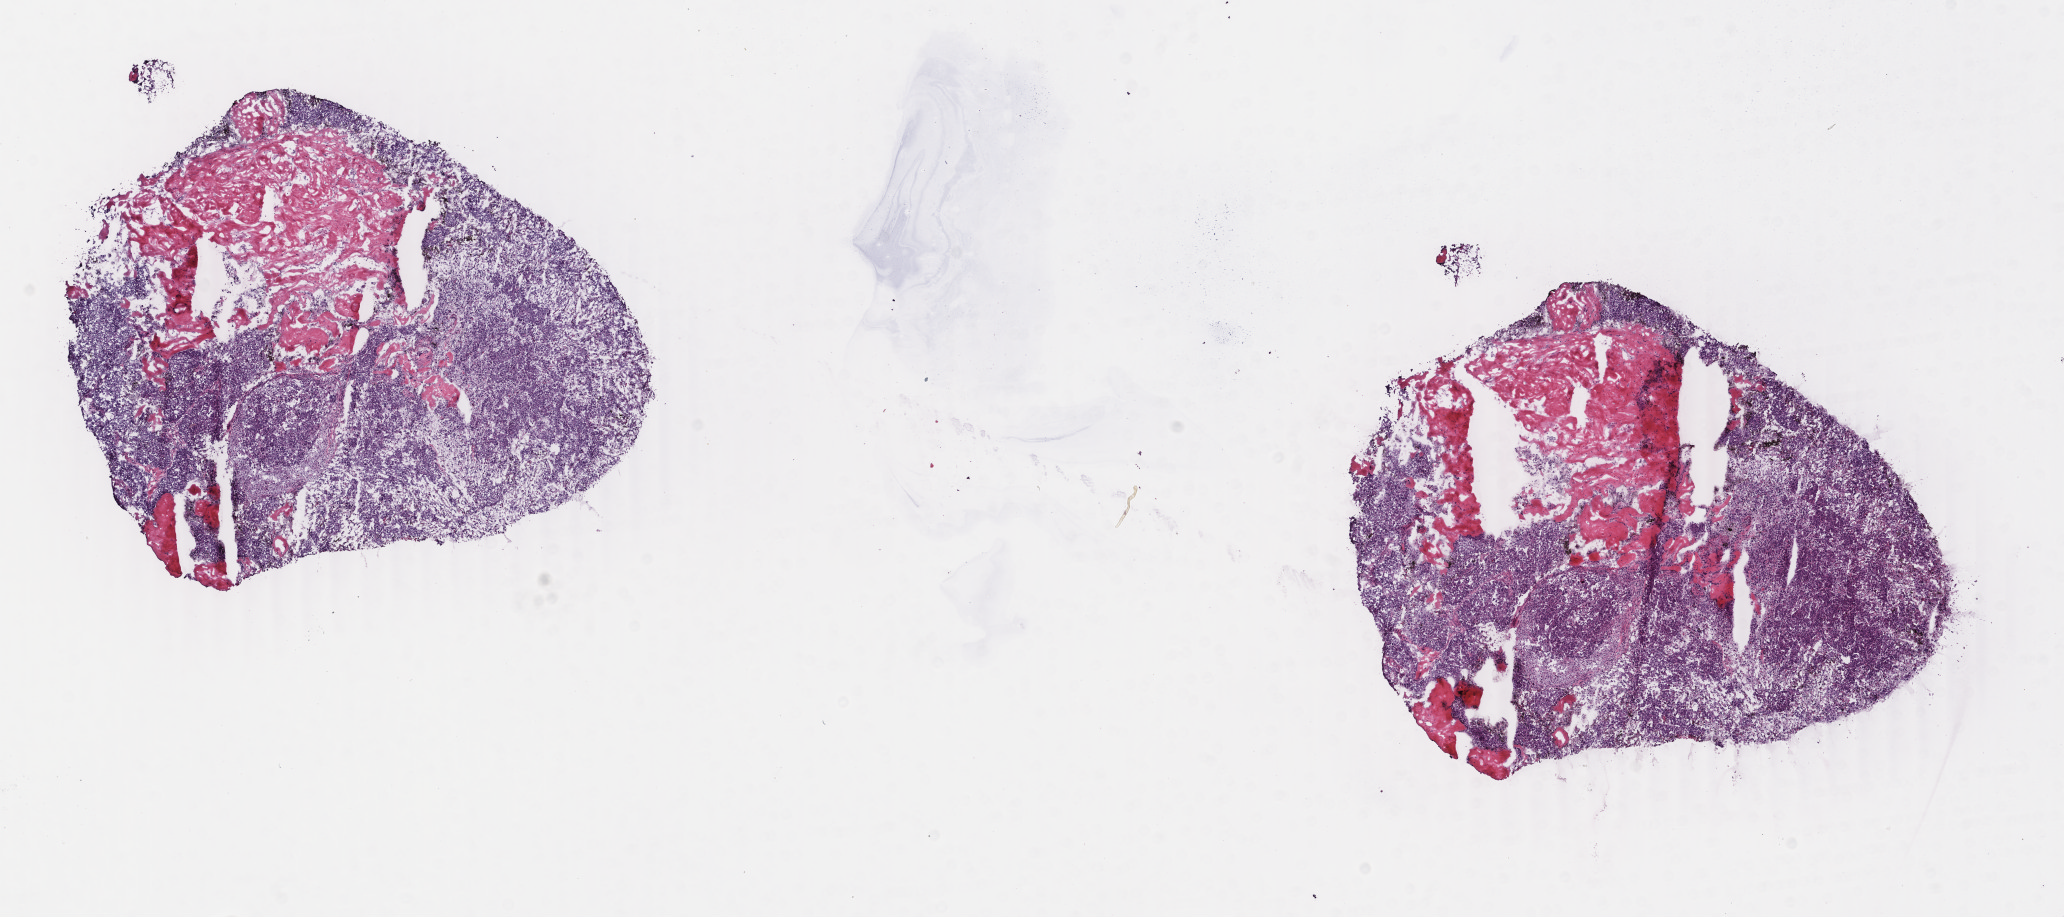
Digitized H&E tissue section (whole slide) — a low-resolution overview of the entire scanned area, about 16.4 x 7.3 mm (acquisition: 40x scan), frozen section from the bottom of the tissue portion, uterus, primary tumour sample. Female, age 74 years at initial diagnosis. Histologic grade: G3 (poorly differentiated). Slide review estimates, as recorded: tumour cells 30%, tumour nuclei 90%, normal cells 0%, stromal cells 10%, necrosis 60%. Infiltration values recorded for this section: lymphocyte infiltration 50%, monocyte infiltration 20%, neutrophil infiltration 50%.
* lymph nodes positive (case pathology): 0 of 24 examined
* FIGO stage: IB
* pathologic diagnosis: Endometrioid adenocarcinoma, NOS (endometrium)